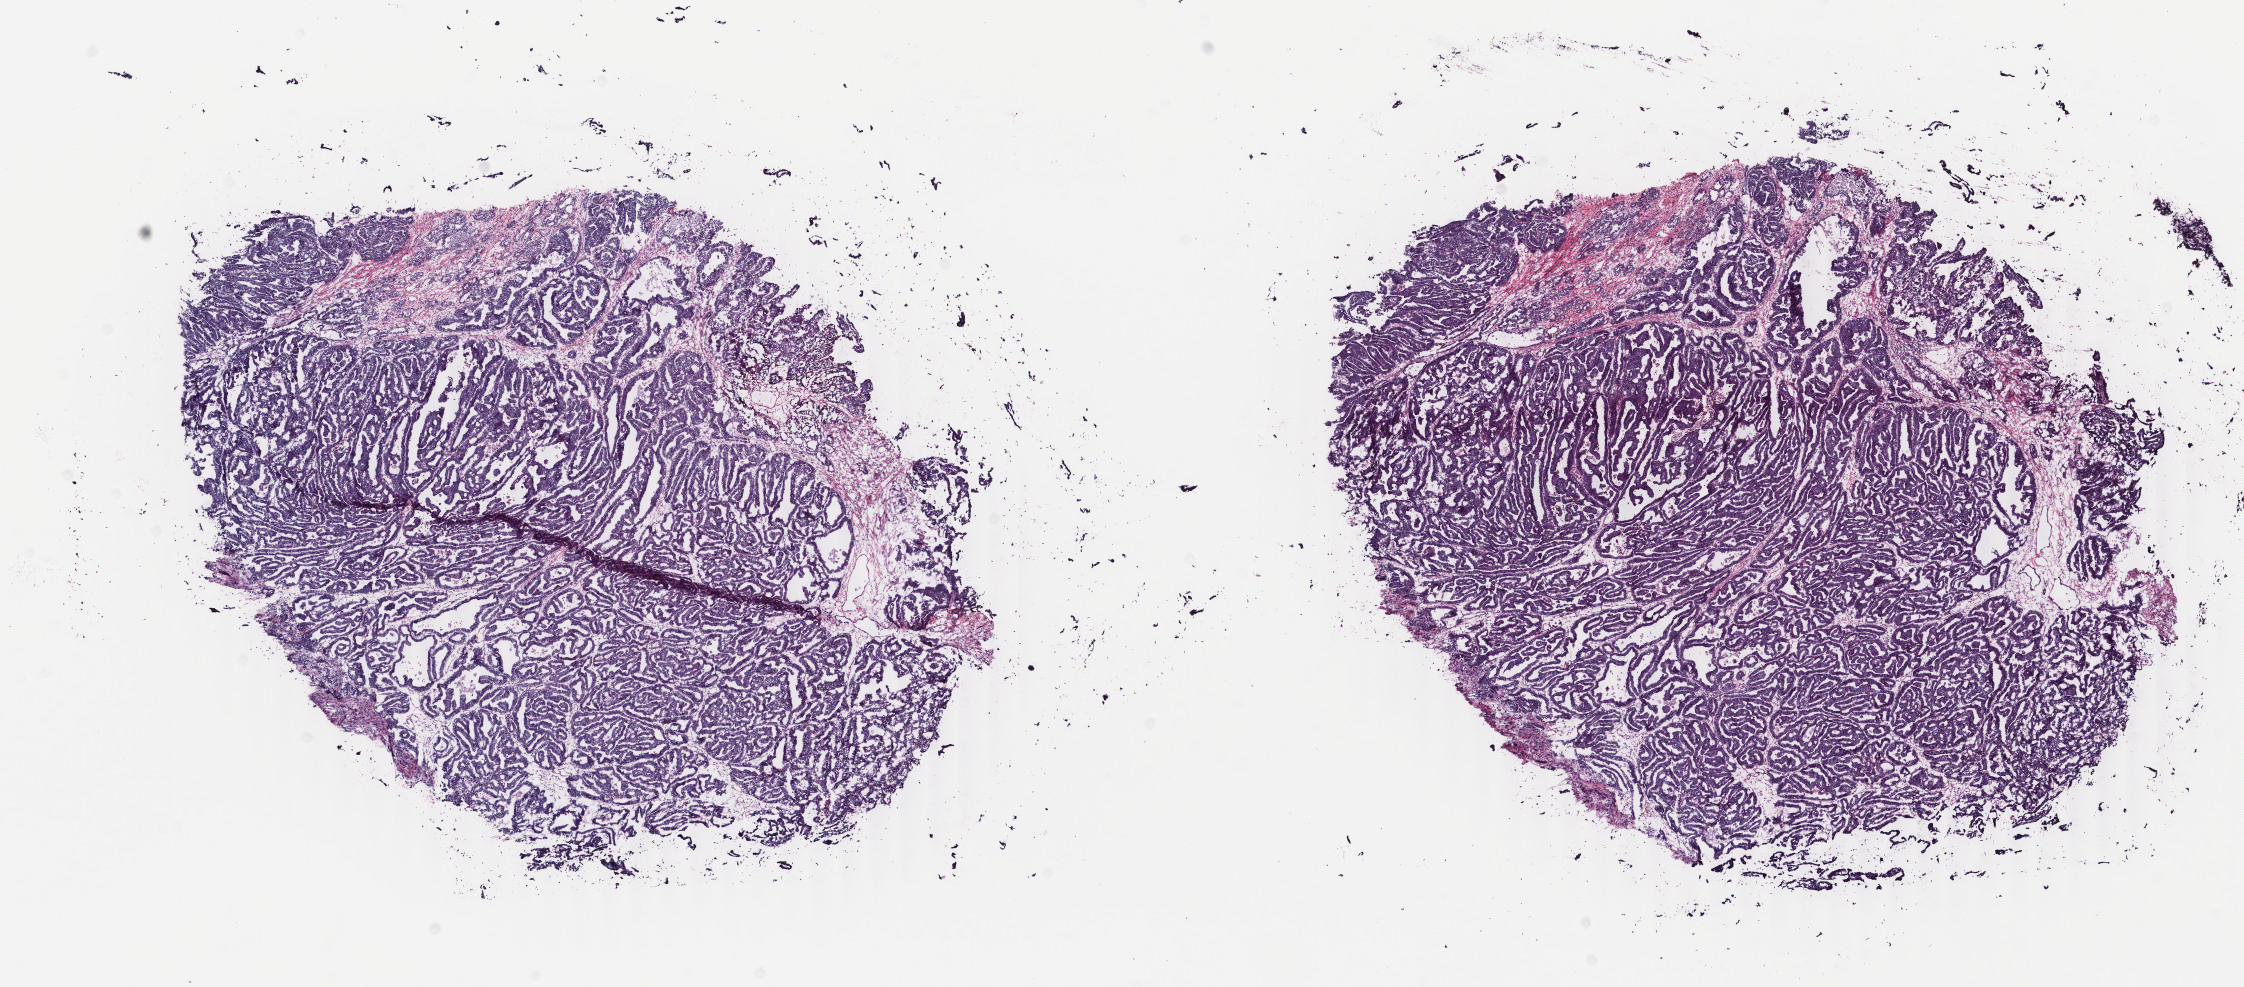
Whole-slide histology image, H&E-stained, low-resolution overview of the scanned area, about 17.8 x 7.8 mm (slide scanned at 40x), frozen section from the bottom of the tissue portion, primary tumour sample from the uterus. Patient: female, age at initial diagnosis 80 years. Histologic grade: G3 (poorly differentiated). Pathologist review of this section (percent, as recorded): tumour cells 85%, tumour nuclei 75%, normal cells 0%, stromal cells 15%, necrosis 0%. Inflammatory infiltration, as recorded: lymphocyte infiltration 0%, monocyte infiltration 0%, neutrophil infiltration 0%.
Pathologic diagnosis: Endometrioid adenocarcinoma, NOS (endometrium). FIGO stage: IB.